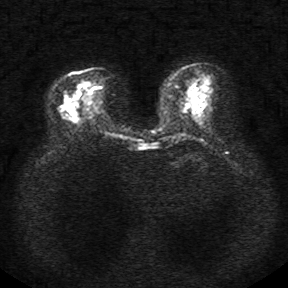
Breast MRI, one axial slice. Position 9 of 34 along the scan axis. Diffusion-weighted series; image 2 of 4 stored at this slice position (different b-values; order by instance number). 1.5 T. 5 mm slice thickness. 288 × 288 image matrix. Female patient.
Outlined on this slice (outlined manually by an expert reader):
- tumour on diffusion-weighted imaging: bounding box [x1, y1, x2, y2] px = [80, 84, 88, 87]